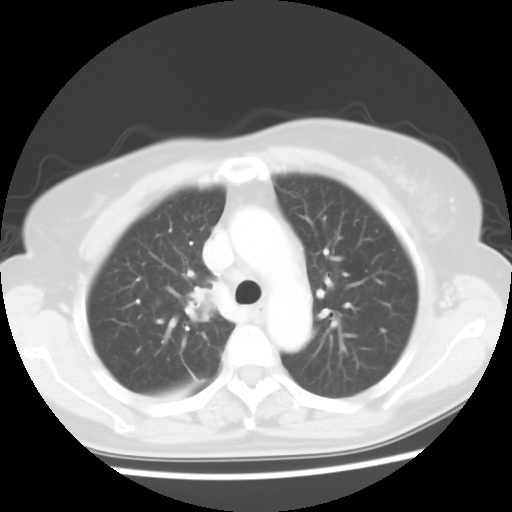
Chest CT, one axial slice; reconstruction kernel STANDARD; 120 kVp; lung window (W 1500 / L -600 HU); 5 mm slice thickness; 512 × 512 image matrix, field of view 314 × 314 mm. Patient: female, 62 years. From the clinical record (not read from this slice): clinical TNM (as recorded): T2 N1 M1a.
Outlined on this slice (rectangle marked by the reading radiologist):
- lung tumour (recorded histology: adenocarcinoma): bounding box (x1, y1, x2, y2) in pixels: (178, 278, 223, 325)